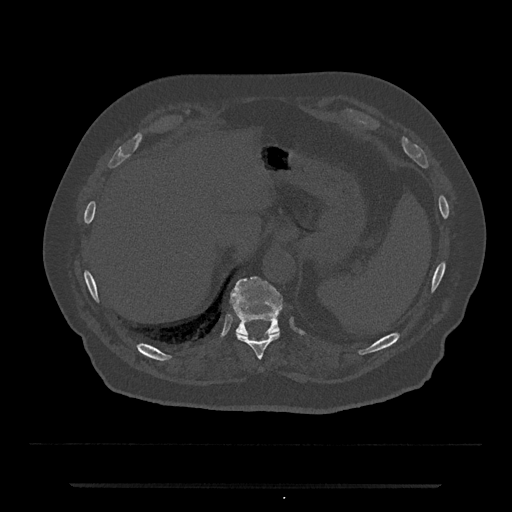
CT including the spine, one axial slice. Position 683 of 797 along the scan axis. Bone window (W 1800 / L 400 HU). 0.5 mm slice thickness. 512 × 512 image matrix, field of view 434 × 434 mm. Patient: male, 80 years. Case-level facts recorded for this patient, not image findings: primary cancer: prostate.
Structures marked on this image (semi-automatically segmented with operator editing):
- T10 vertebra: box from (x=236, y=331) to (x=280, y=360) px
- T11 vertebra: (x=230, y=276)–(x=283, y=336)